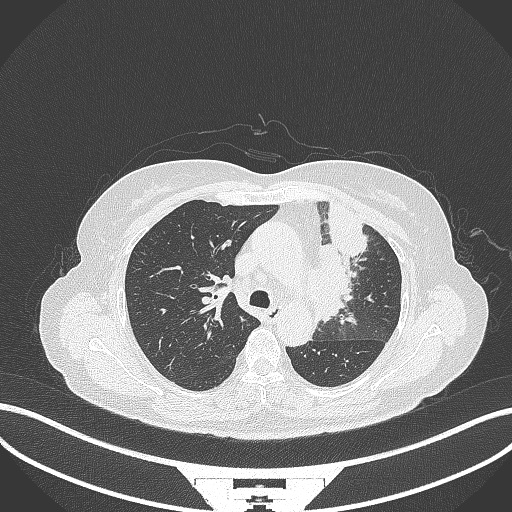
Chest CT, one axial slice; slice 228 of 382 in the series (ordered by position); reconstruction kernel B70f; 120 kVp; lung window (W 1500 / L -600 HU); 512 × 512 image matrix, field of view 400 × 400 mm. Patient: female, 64 years. From the clinical record (not read from this slice): clinical TNM (as recorded): T2a N2 M0.
Annotated regions visible in this slice (bounding box drawn by a radiologist):
- lung tumour (recorded histology: adenocarcinoma): bounding box (x1, y1, x2, y2) in pixels: (305, 203, 369, 325)